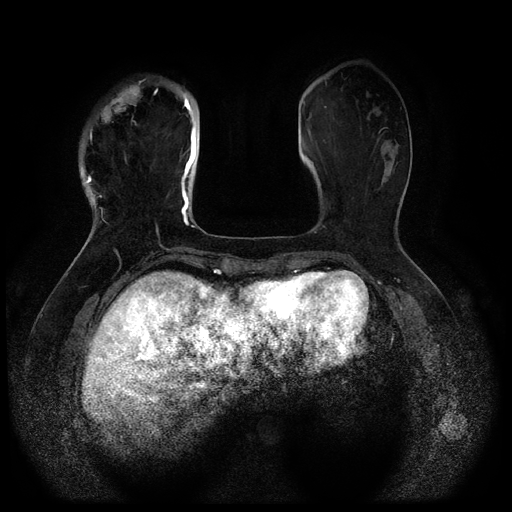
Breast MRI (dynamic contrast-enhanced, multi-phase), one axial slice; slice 28 of 116 in the series (ordered by position); dynamic contrast-enhanced series, time point 2 of 5 at this slice position (early post-contrast); 1.5 T; TE 2.6 ms, TR 5.3 ms; 2 mm slice thickness; 512 × 512 image matrix, field of view 350 × 350 mm. Patient: female, 51 years.
Structures marked on this image (semi-automatic segmentation, software-assisted and operator-edited):
- breast lesion (labelled 'tumour' in the annotation; benign lesions carry a separate 'benign' label): bounding box (x1, y1, x2, y2) in pixels: (96, 83, 142, 126)